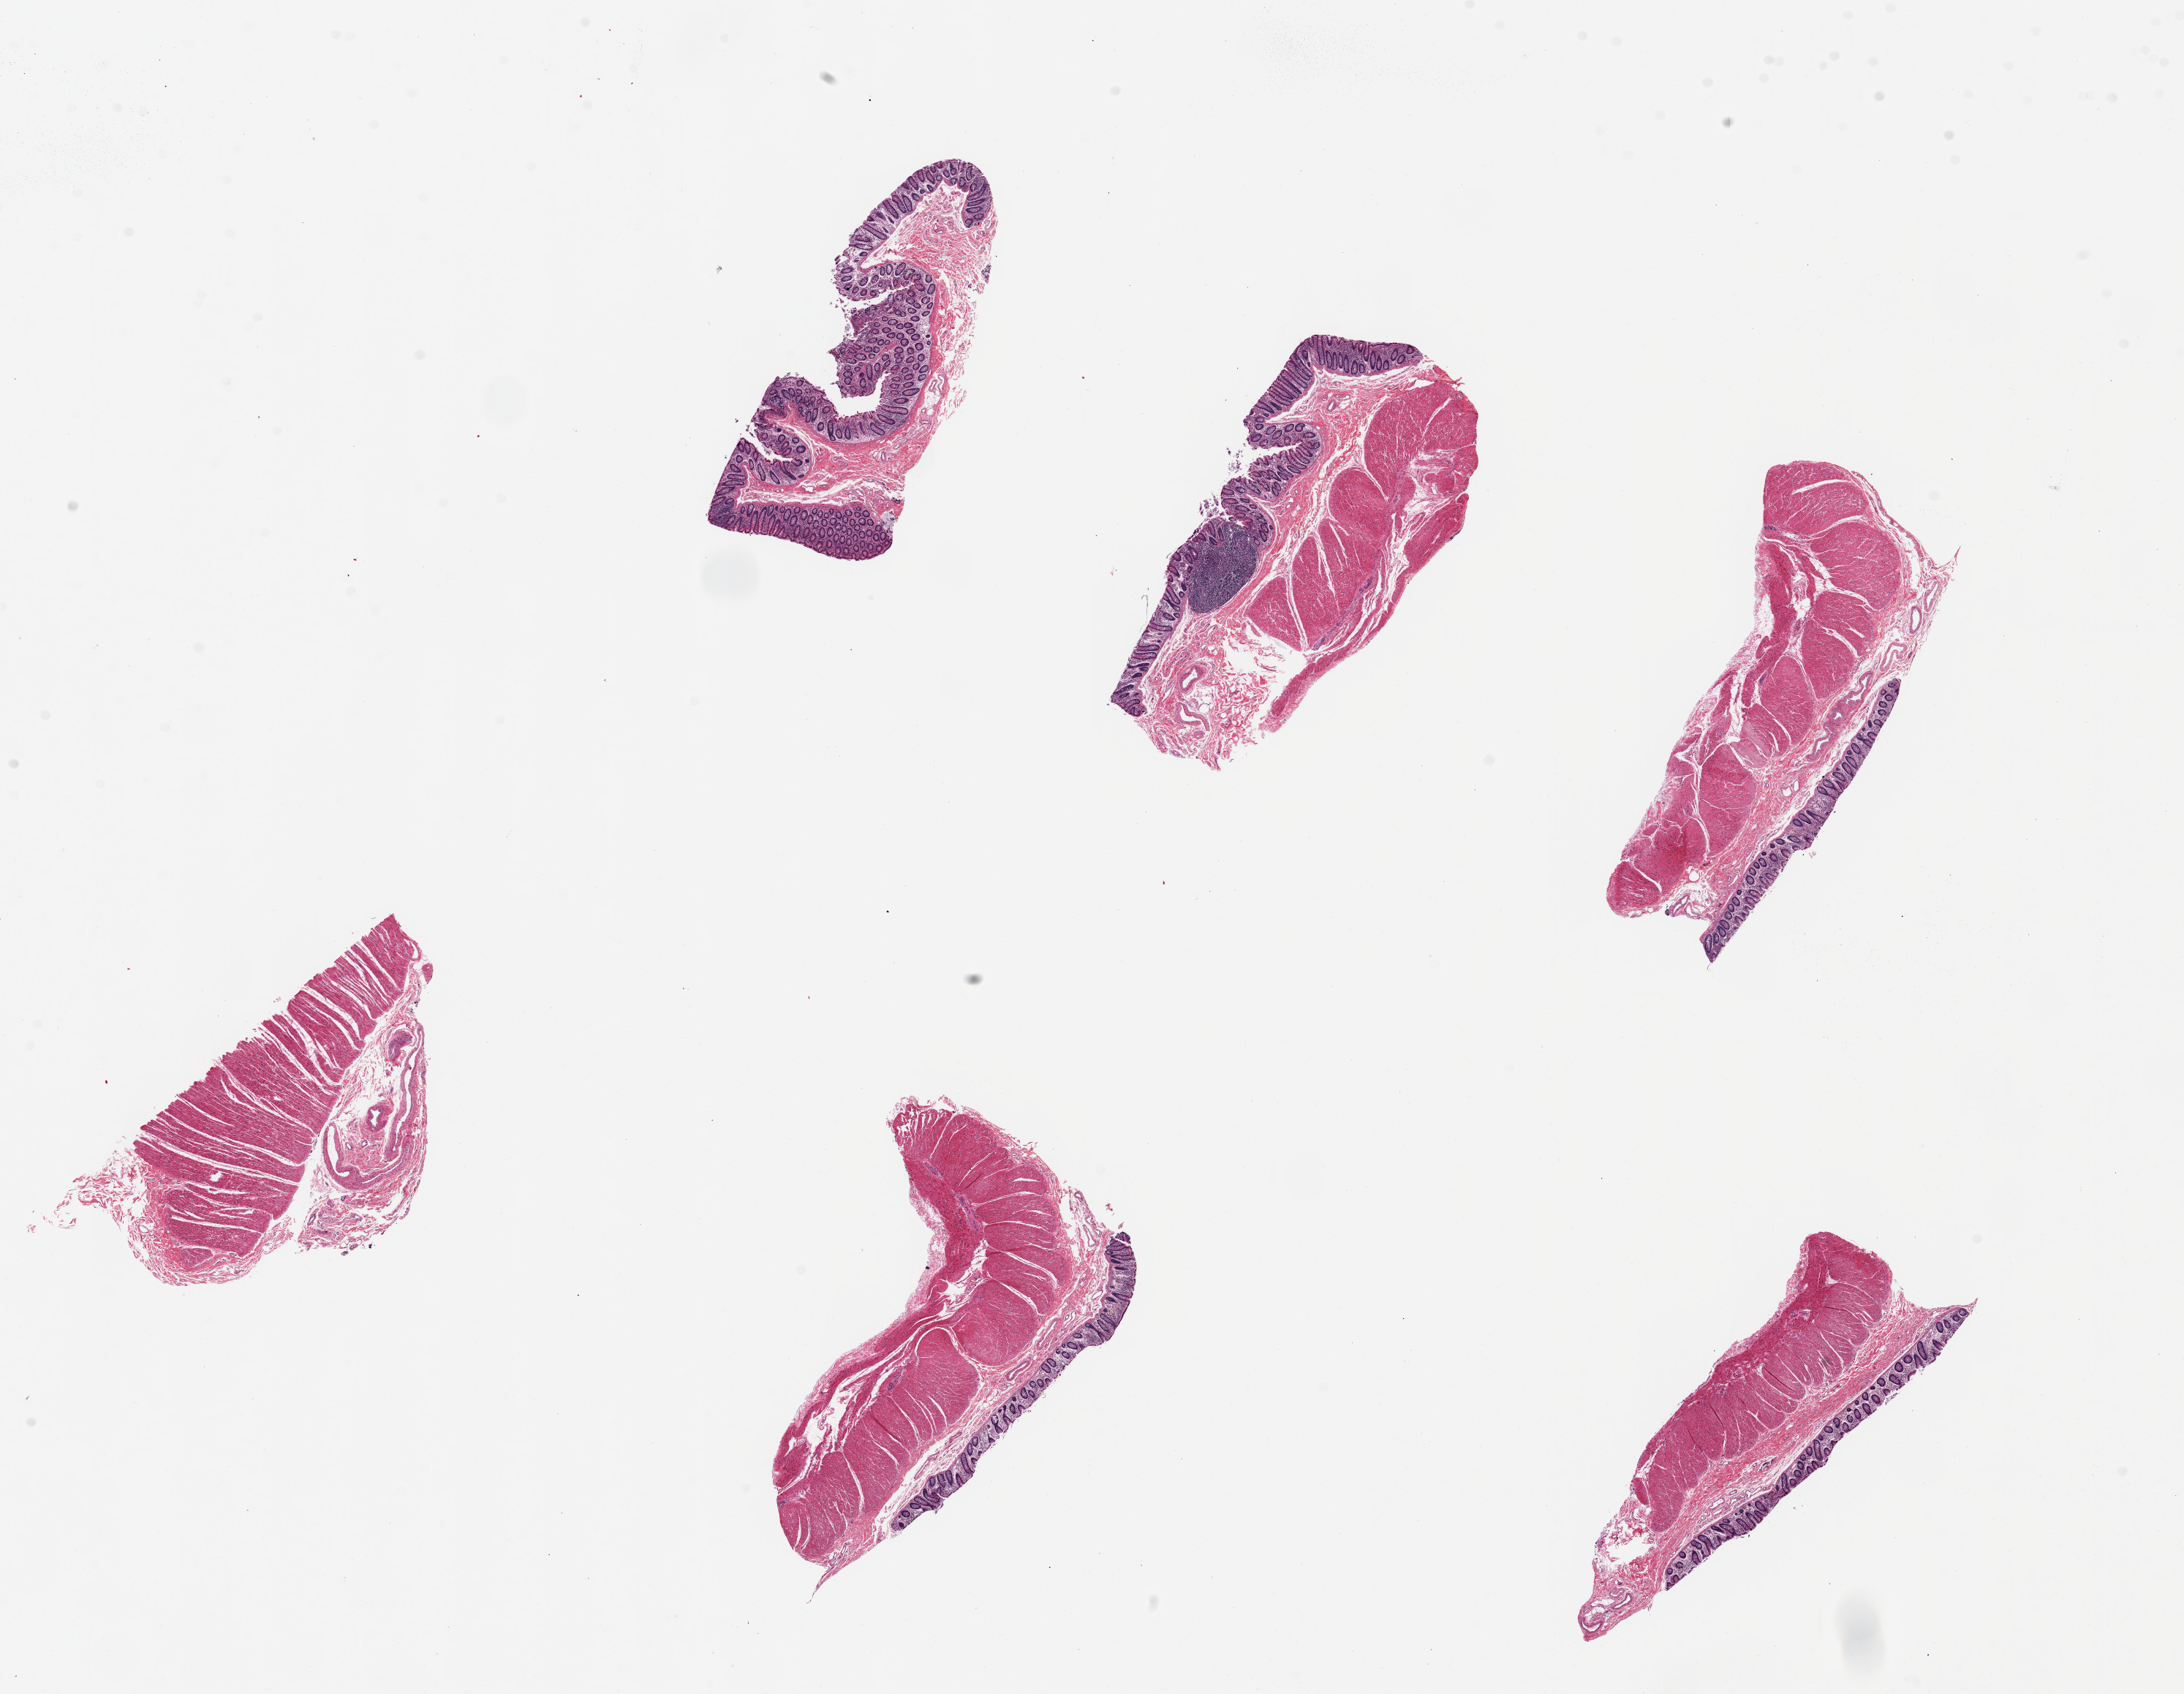
Digitized hematoxylin and eosin (H&E)-stained section, whole scanned area (about 23.6 x 18.3 mm) shown as a low-resolution overview, PAXgene-fixed paraffin-embedded (PFPE) section, section of transverse colon (target tissue), donor tissue sample. Donor sex: male.
- review note (as recorded): 6 pieces, up to 5.5x2mm; 1 of 6 has muscularis only, other 5 have full thickness